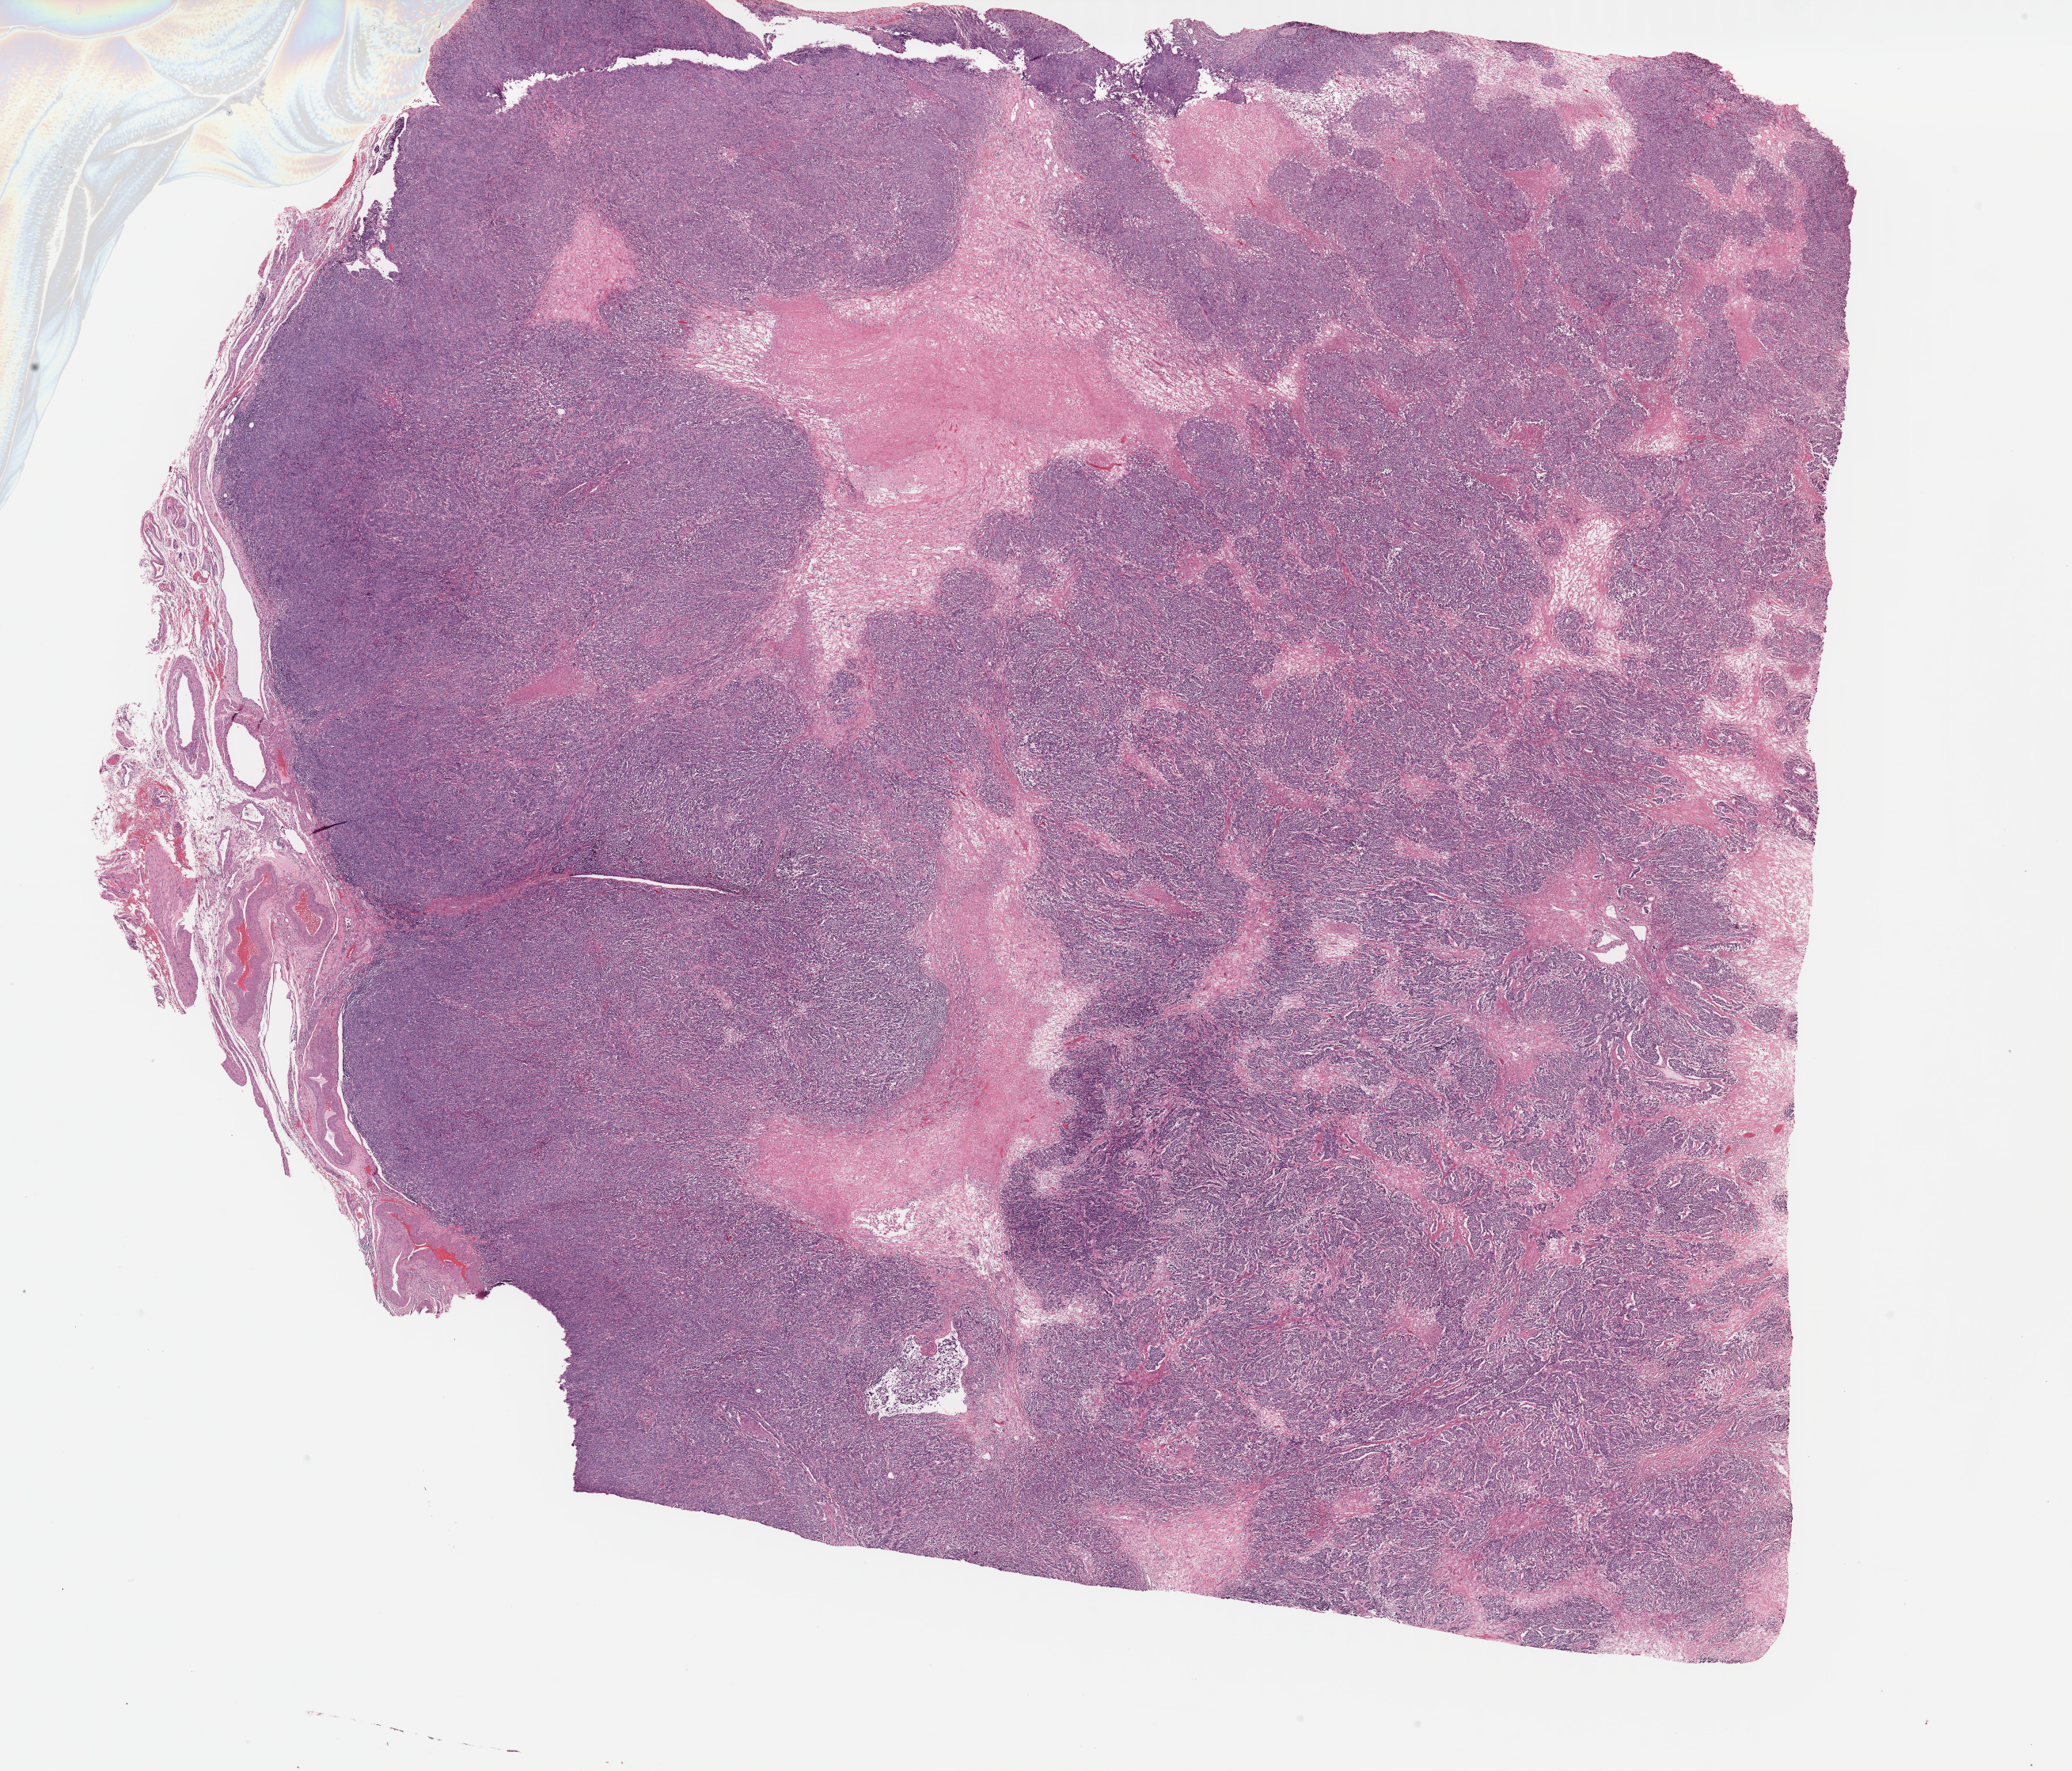
Whole-slide histology image, H&E, shown as a low-resolution overview of the whole scanned area (about 20.7 x 17.7 mm, from a 40x scan), formalin-fixed paraffin-embedded (FFPE) diagnostic section, primary tumour sample from the uterus. Female, age 59 years at initial diagnosis. Histologic grade: G3 (poorly differentiated).
FIGO stage: IVA. Histologic diagnosis: Endometrioid adenocarcinoma, NOS (endometrium).